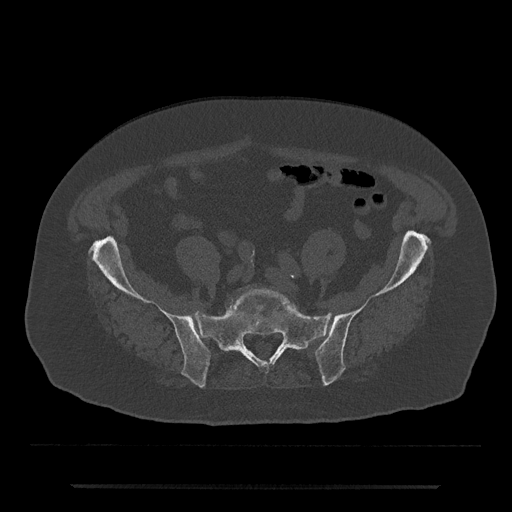
CT including the spine, one axial slice; slice 242 of 797 in the series (ordered by position); bone window (W 1800 / L 400 HU); 512 × 512 image matrix, field of view 434 × 434 mm. Male patient, age 80 years. Case-level facts recorded for this patient, not image findings: primary cancer: prostate; vertebrae with lytic lesions (as recorded): L1, T11.
Annotated regions visible in this slice (semi-automatic segmentation, software-assisted and operator-edited):
- L5 vertebra: bounding box [x1, y1, x2, y2] px = [230, 288, 299, 313]